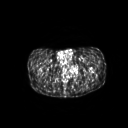
FDG PET of an extremity soft-tissue mass (from a PET/CT study), one axial slice; position 44 of 267 along the scan axis; 3.27 mm slice thickness; 128 × 128 image matrix, field of view 600 × 600 mm. Patient: male, 59 years. From the clinical record (not read from this slice): histological type: pleiomorphic liposarcoma; grade: high; site of the primary tumour: left thigh.
Structures marked on this image (expert contour drawn on MRI and transferred to this co-registered scan by the dataset authors):
- gross tumour volume including surrounding oedema: box from (x=70, y=65) to (x=82, y=77) px